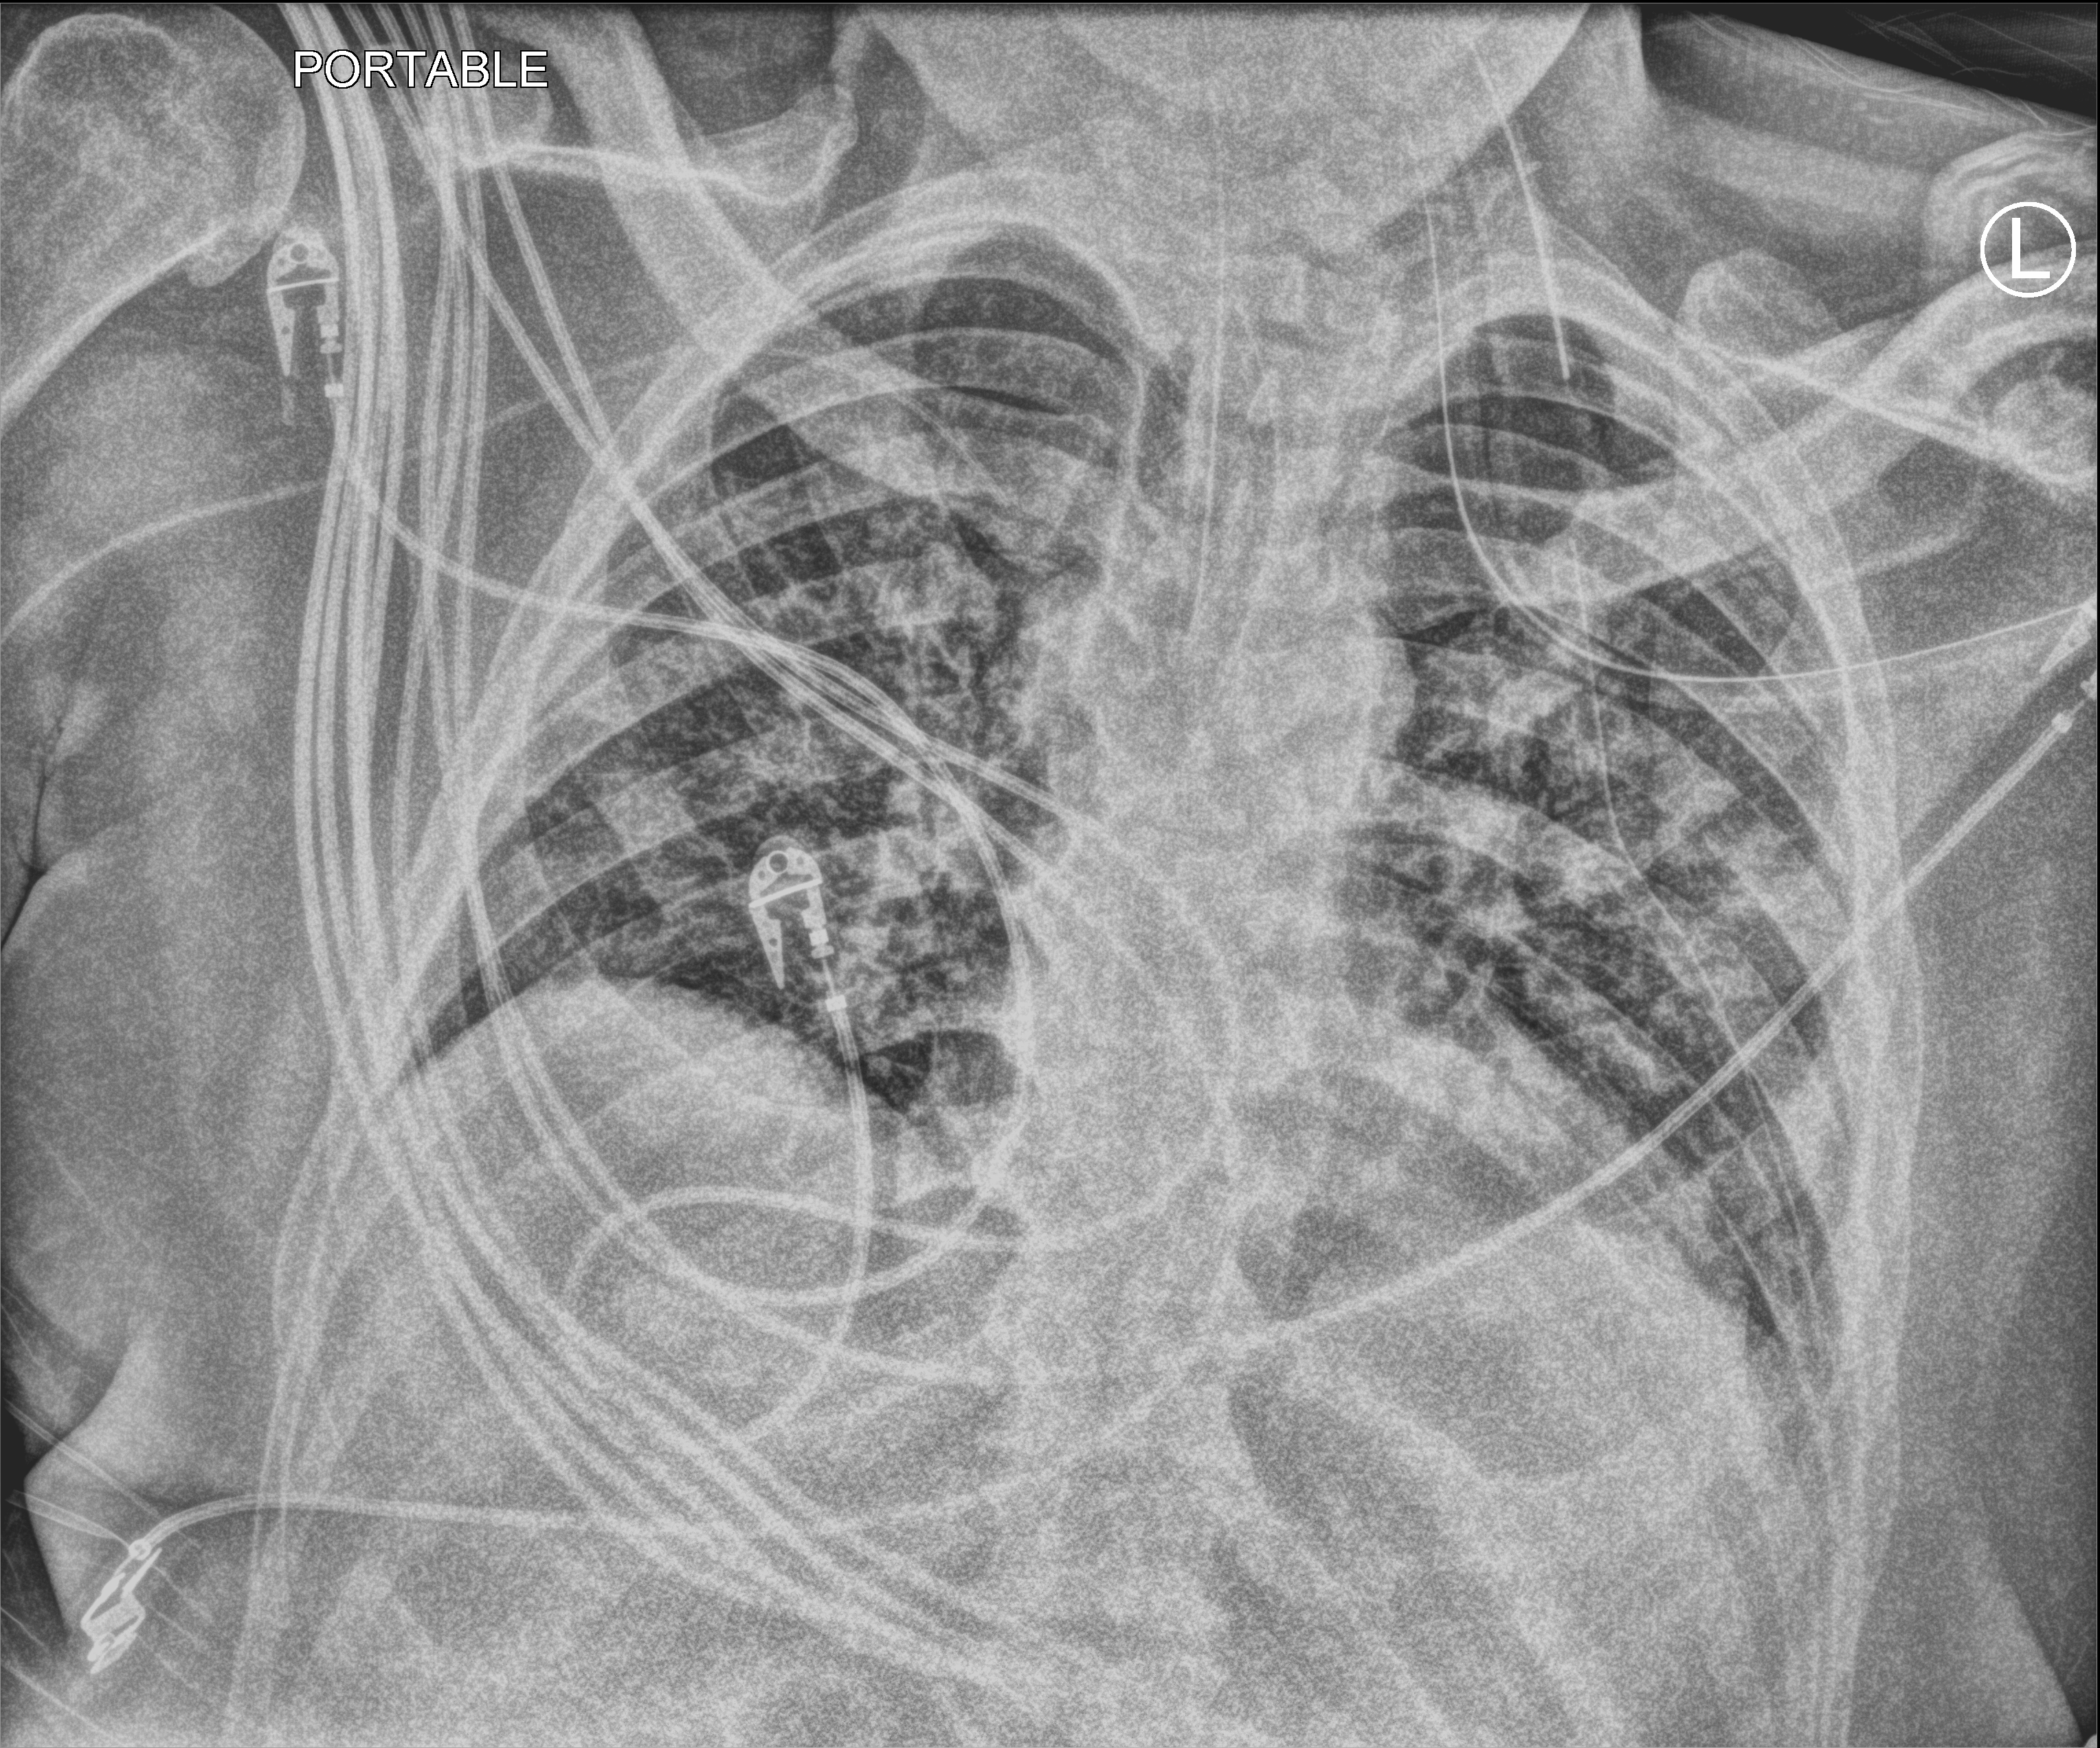
Portable chest radiograph. Patient hospitalised with COVID-19; male, aged 18–59 years.
Admission-level facts for this patient (not findings on this image; timing relative to this image not recorded):
- length of hospital stay: 41 days